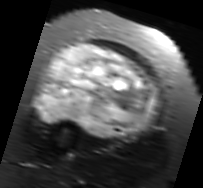
MRI of an extremity soft-tissue mass, one axial slice; slice 41 of 91 in the series (ordered by position); T2-weighted fat-saturated; MR volume resampled by the dataset authors to the PET/CT grid (not the native acquisition matrix); 3.27 mm slice thickness; 203 × 188 image matrix, field of view 198 × 184 mm. Female patient. From the clinical record (not read from this slice): histological type: malignant solitary fibrous tumor; grade: intermediate; site of the primary tumour: right thigh.
Outlined on this slice (expert contour drawn on MRI and transferred to this co-registered scan by the dataset authors):
- gross tumour volume including surrounding oedema: bounding box <33,42,162,139> (left, top, right, bottom; pixels)
- gross tumour volume (mass): <38,42,157,137>